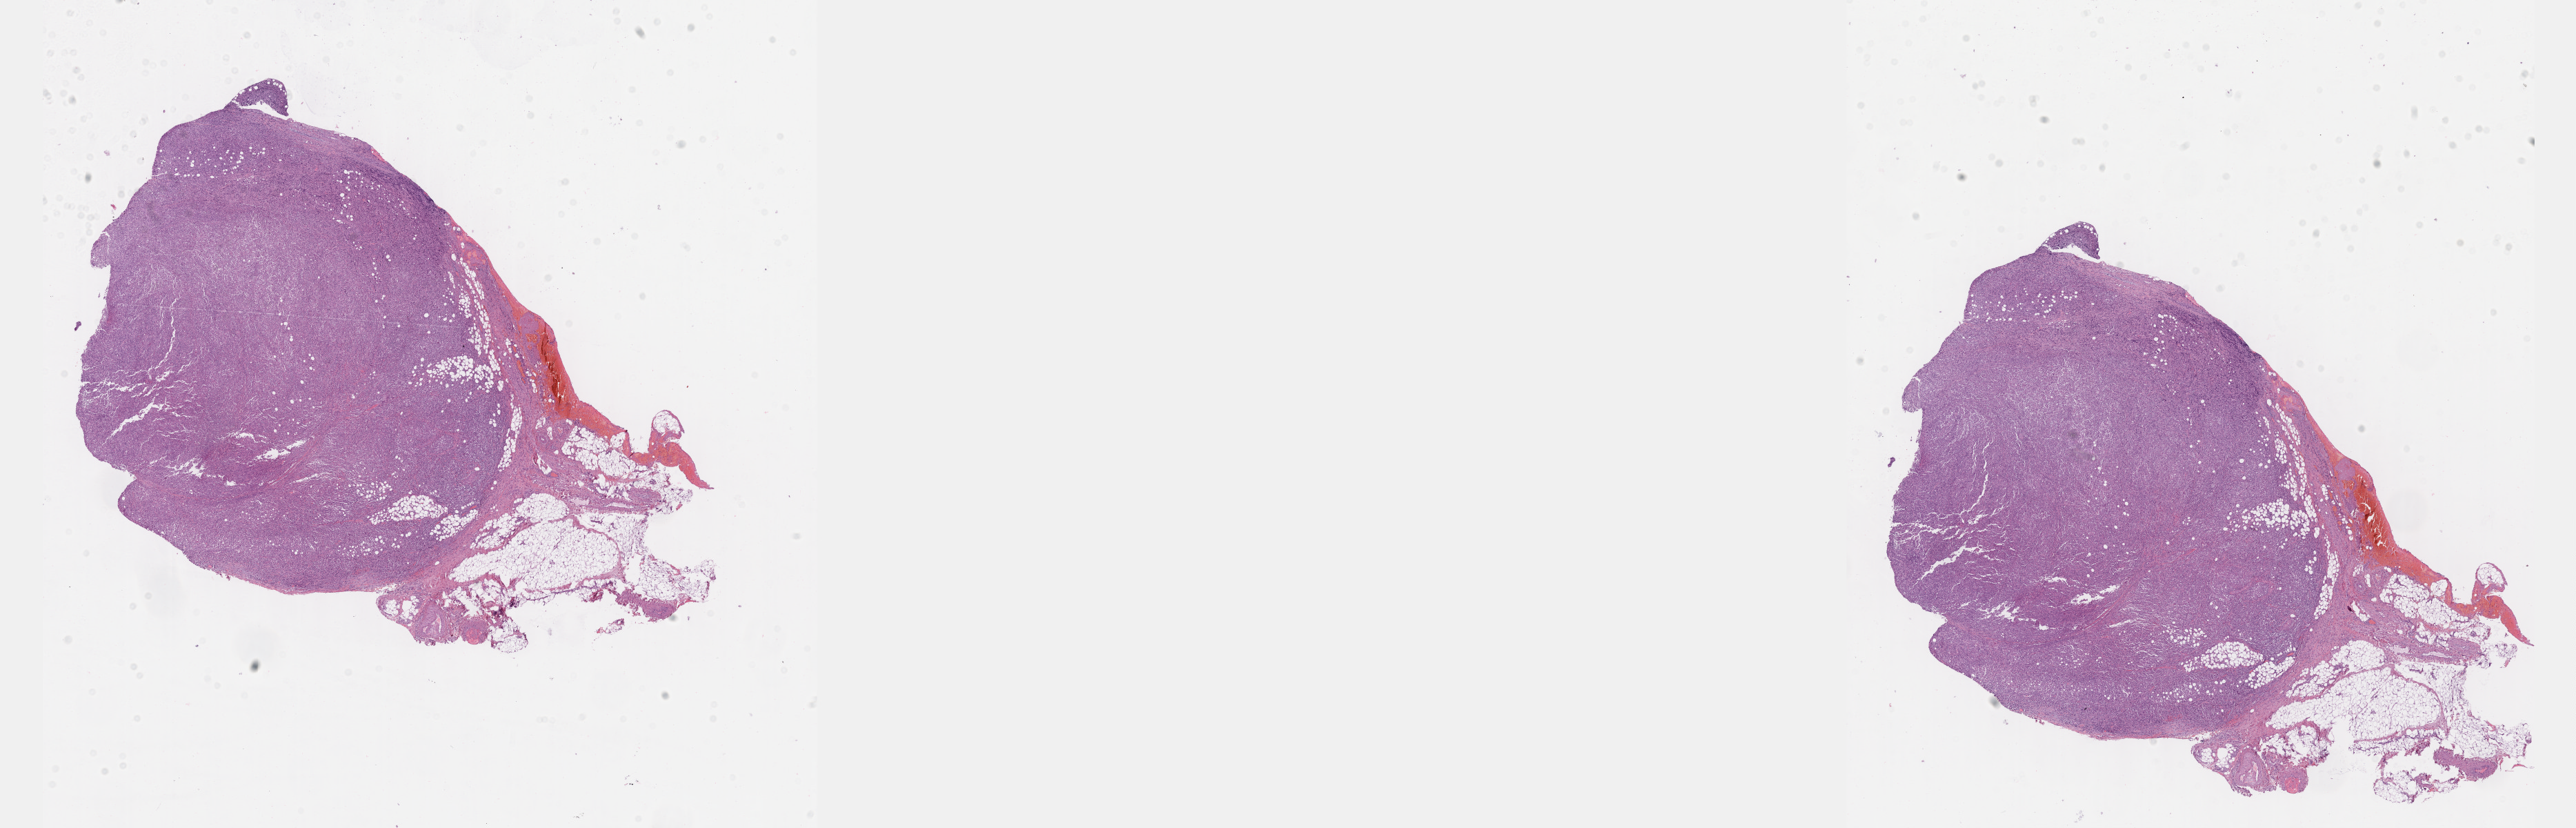
Hematoxylin and eosin (H&E) stained whole-slide image — low-resolution overview of the scanned area, about 30.2 x 9.7 mm (slide scanned at 40x). Formalin-fixed paraffin-embedded (FFPE) diagnostic section. Primary tumour sample from the lymphoid tissue. Female patient; age at initial diagnosis 40 years.
Diagnosis: Mediastinal (thymic) large B-cell lymphoma (lymph nodes of head, face and neck).